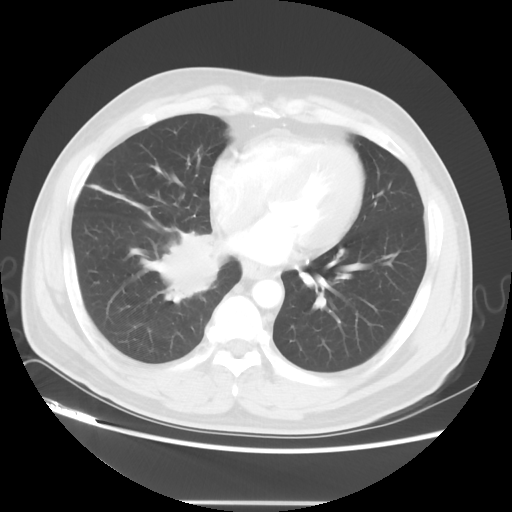
Chest CT, one axial slice. Position 17 of 48 along the scan axis. Reconstruction kernel STANDARD. Lung window (W 1500 / L -600 HU). 512 × 512 image matrix, field of view 390 × 390 mm. Male patient, age 53 years. From the clinical record (not read from this slice): clinical TNM (as recorded): T2 N3 M0; histopathological grade: G3.
Annotated regions visible in this slice (rectangle marked by the reading radiologist):
- lung tumour (recorded histology: small cell carcinoma): box from (x=138, y=222) to (x=225, y=309) px